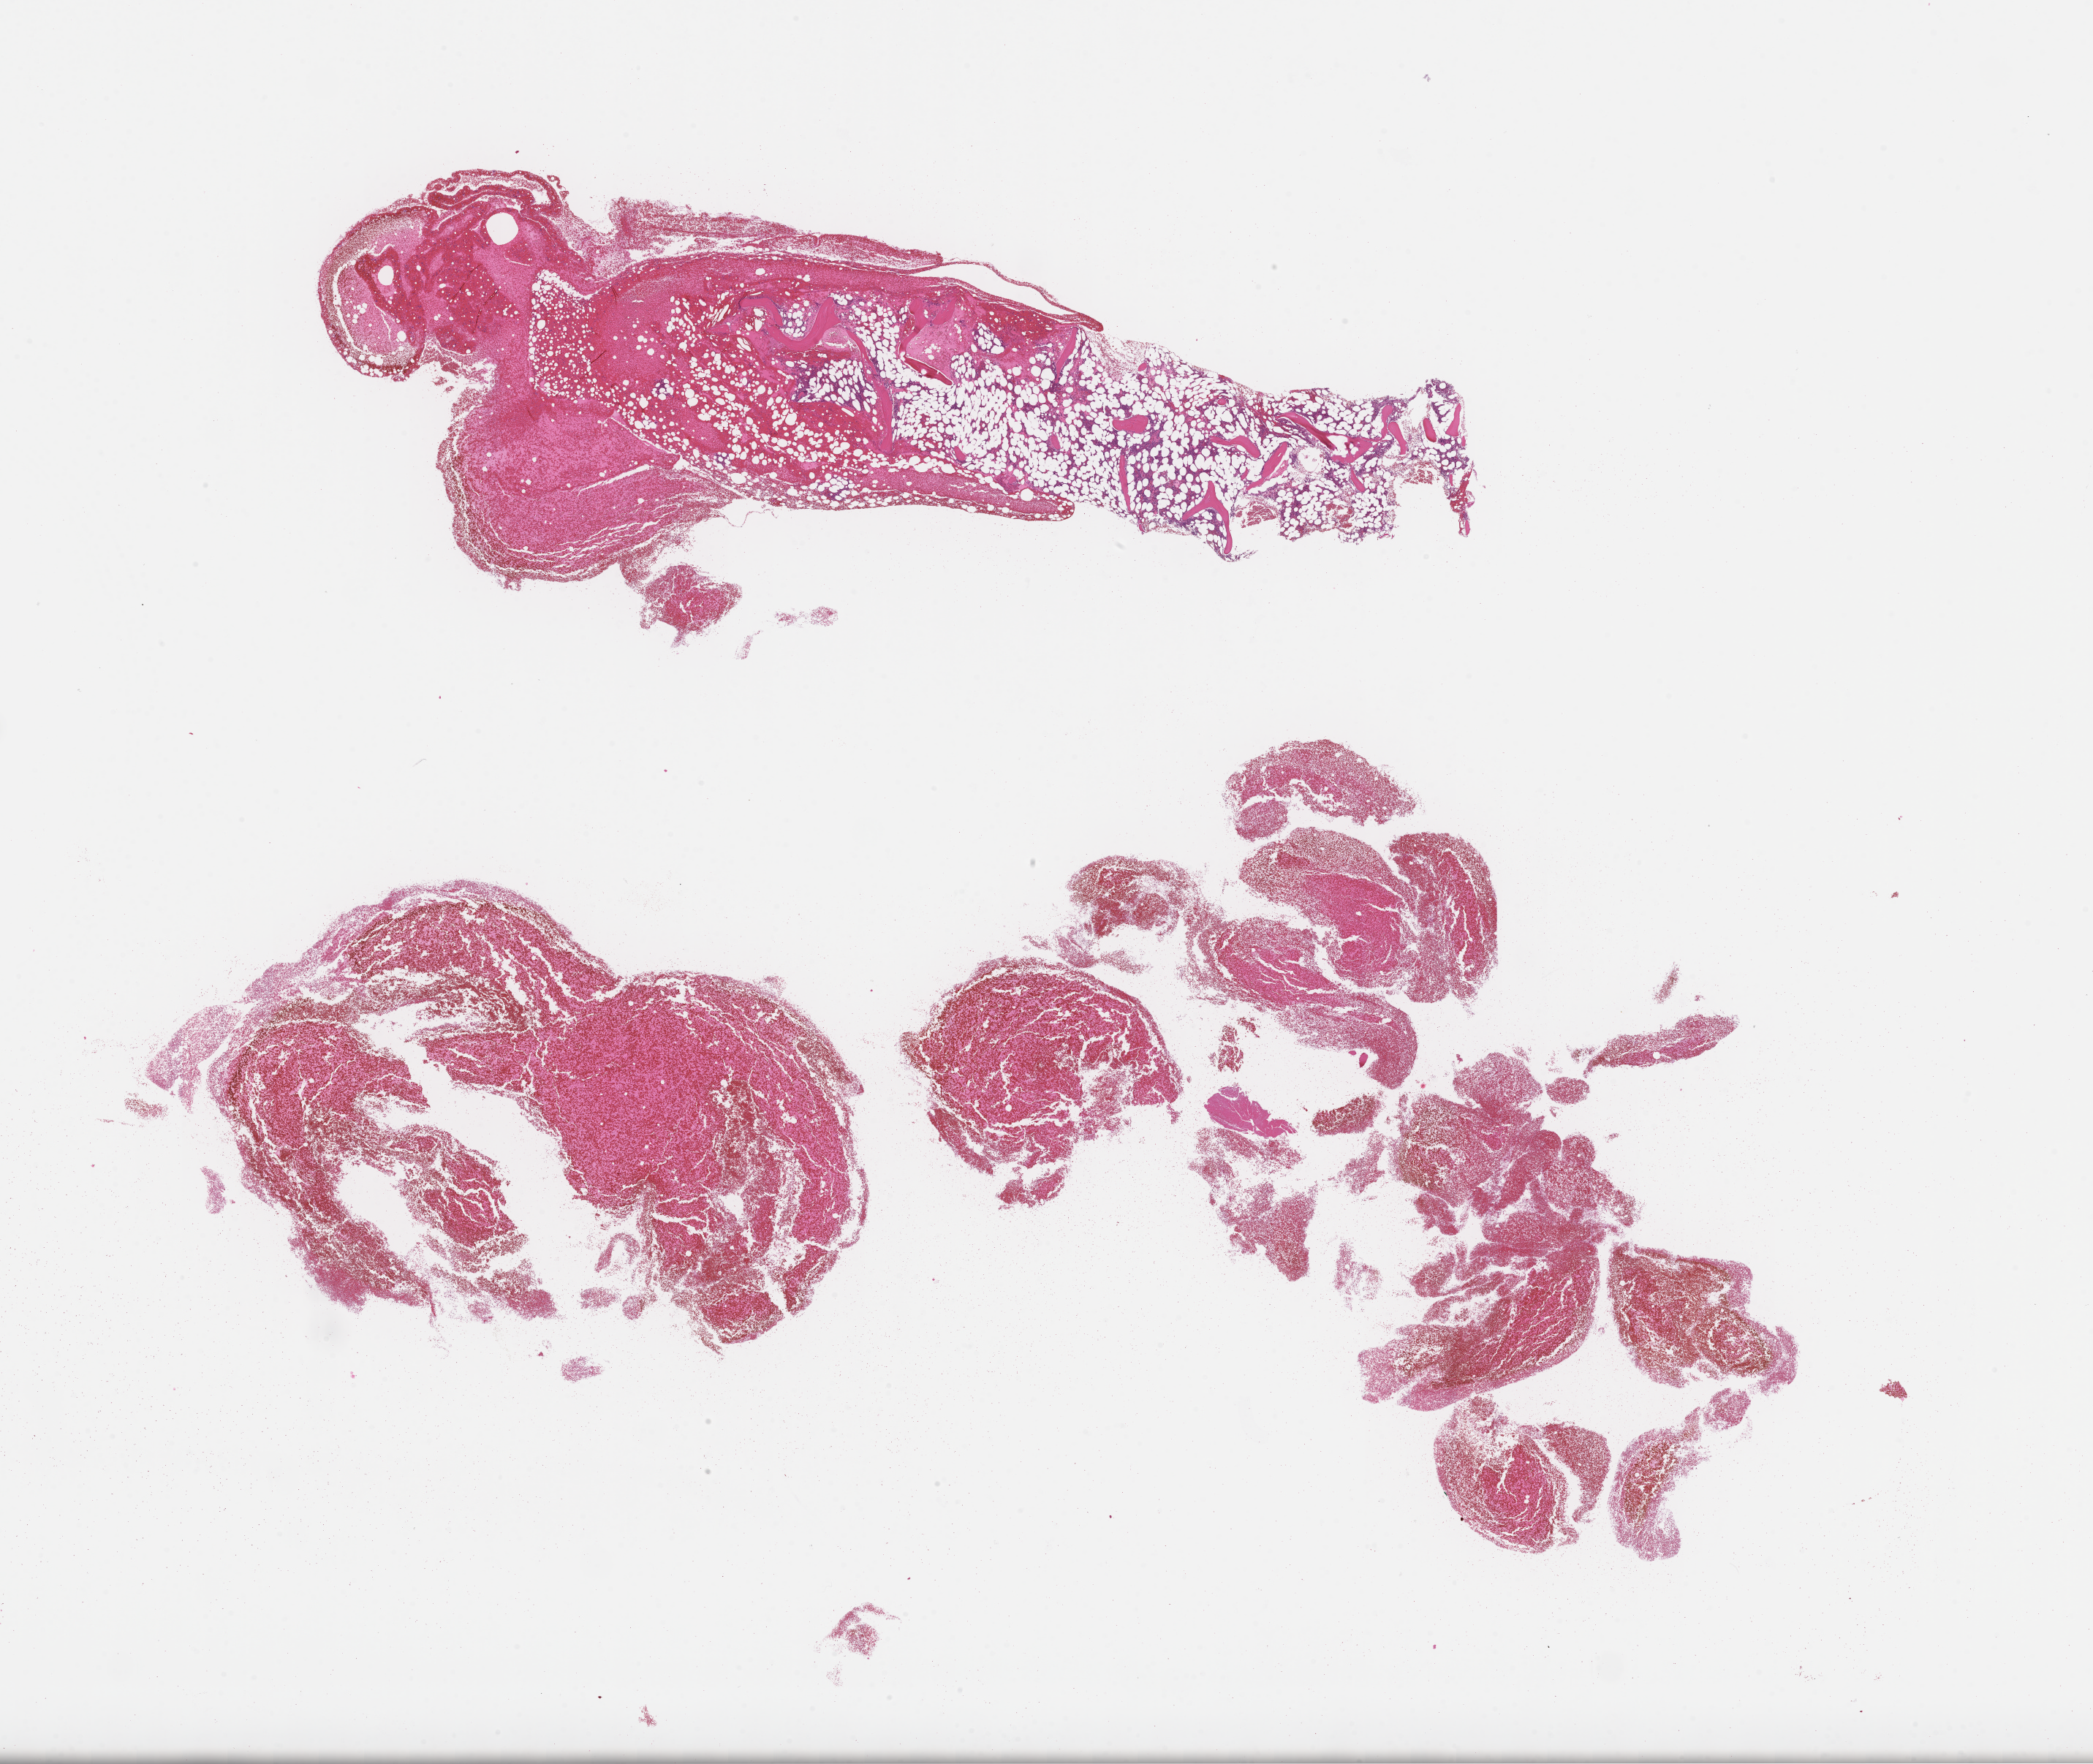
Haematoxylin and eosin whole-slide image — whole scanned area (about 23.1 x 19.5 mm) shown as a low-resolution overview. Formalin-fixed paraffin-embedded section. Site: bone marrow. Specimen time point: archival tissue. Patient sex: male.
• this section: primary tumor
• diagnosis: Plasma Cell Myeloma